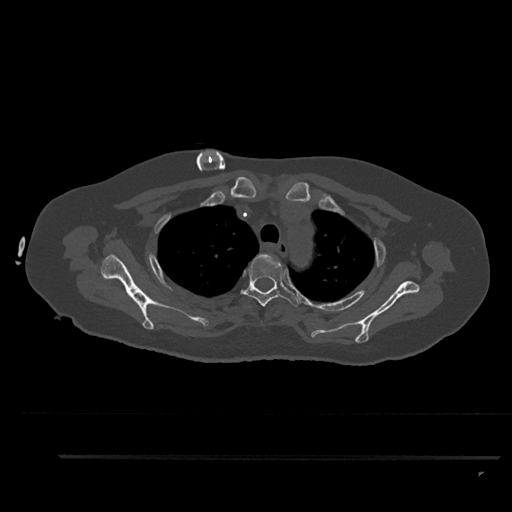
CT including the spine, one axial slice. Slice 688 of 797 in the series (ordered by position). Reconstruction kernel Br40s/3. 120 kVp. Bone window (W 1800 / L 400 HU). 512 × 512 image matrix, field of view 408 × 408 mm. Patient: female, 44 years. Case-level facts recorded for this patient, not image findings: primary cancer: renal; vertebrae with lytic lesions (as recorded): L1.
Outlined on this slice (semi-automatic segmentation, software-assisted and operator-edited):
- T3 vertebra: bounding box (x1, y1, x2, y2) in pixels: (241, 254, 300, 307)